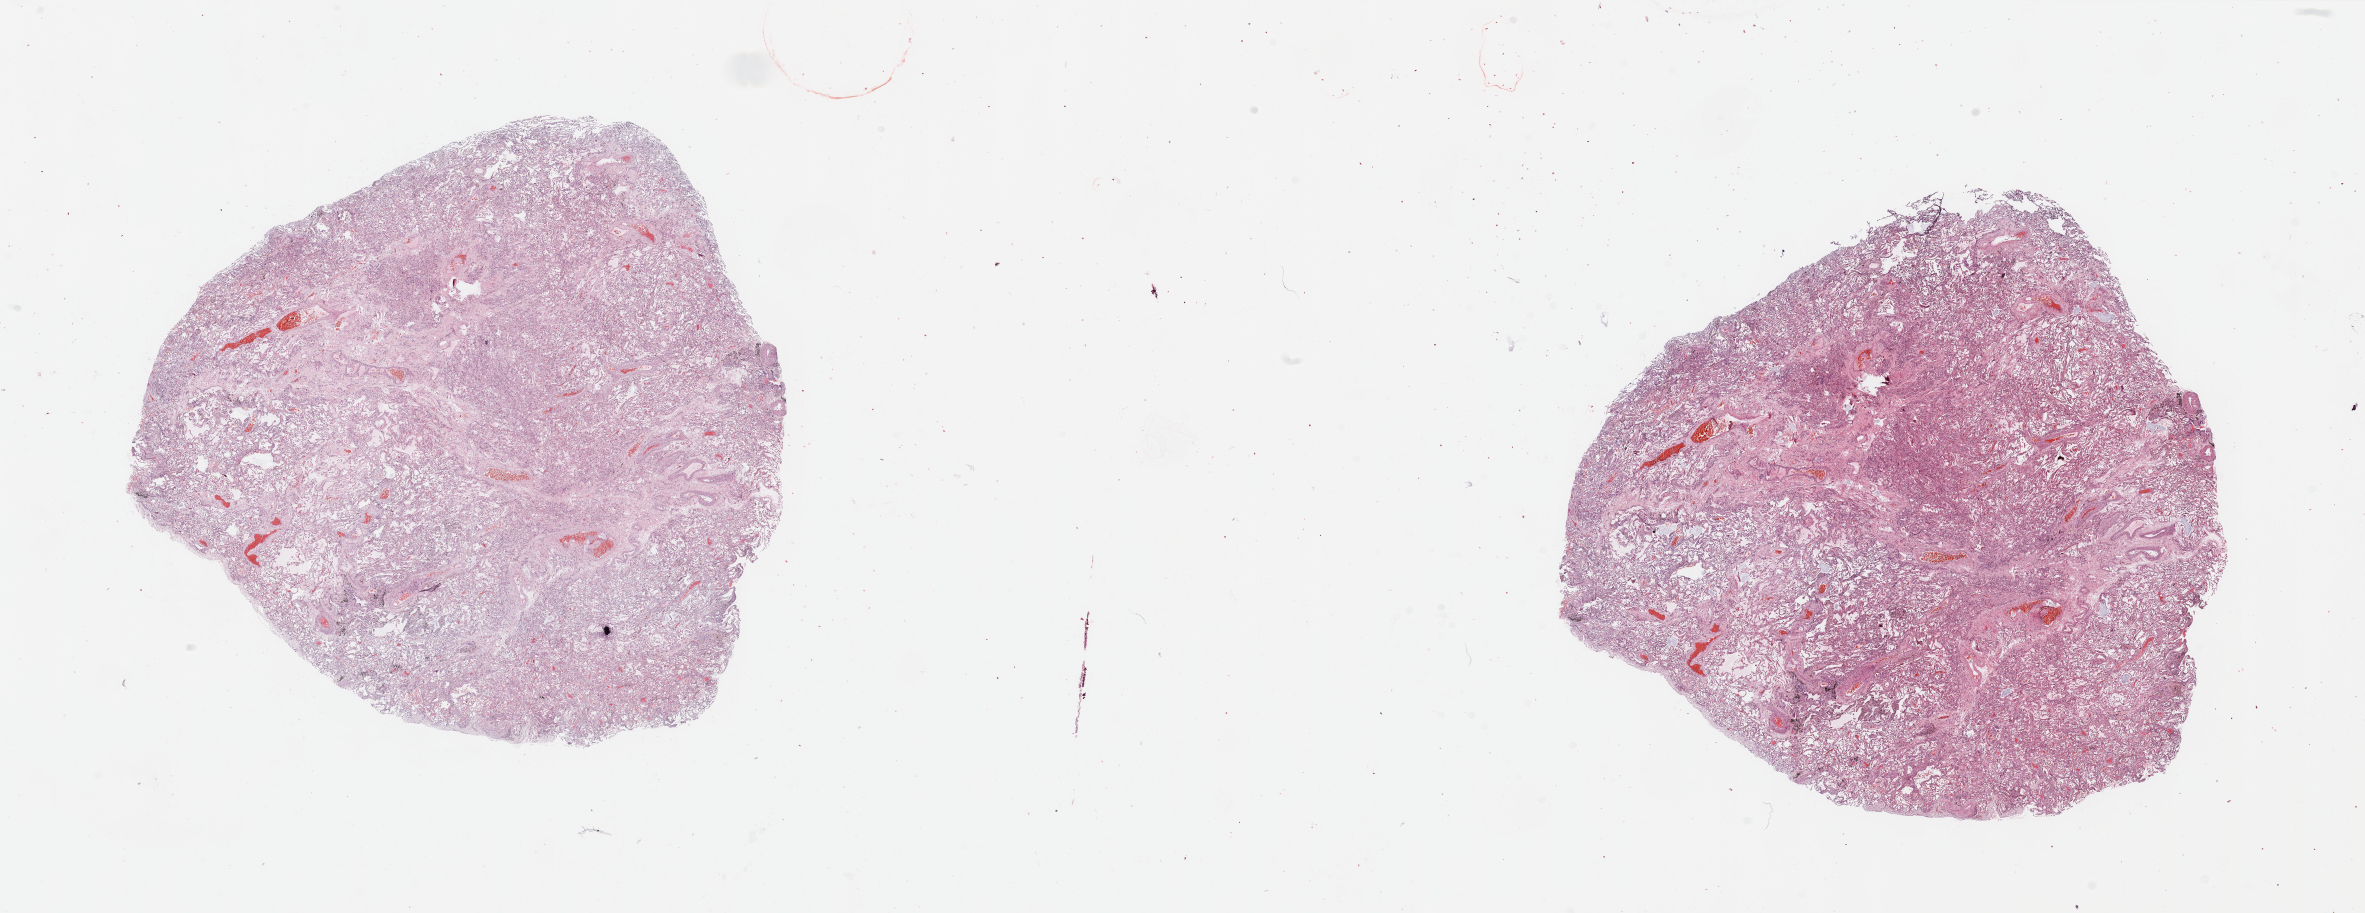
Whole-slide histology image, H&E-stained, low-resolution overview of the scanned area, about 37.4 x 14.4 mm; normal (non-tumour) tissue sample, sampled site: lung. 65-year-old male patient.
This section: normal (non-tumour) tissue from the same patient. Patient diagnosis: Squamous cell carcinoma, NOS.